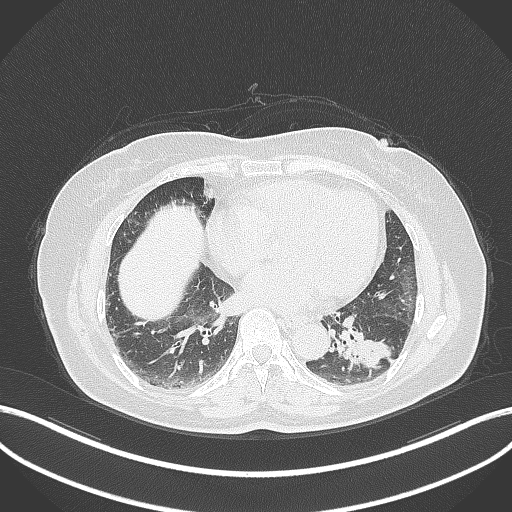
Chest CT, one axial slice. Slice 147 of 311 in the series (ordered by position). 120 kVp. Lung window (W 1500 / L -600 HU). 512 × 512 image matrix, field of view 400 × 400 mm. Female patient, age 59 years. From the clinical record (not read from this slice): clinical TNM (as recorded): T2a N0 M0.
Annotated regions visible in this slice (bounding box drawn by a radiologist):
- lung tumour (recorded histology: adenocarcinoma): box from (x=332, y=325) to (x=393, y=369) px